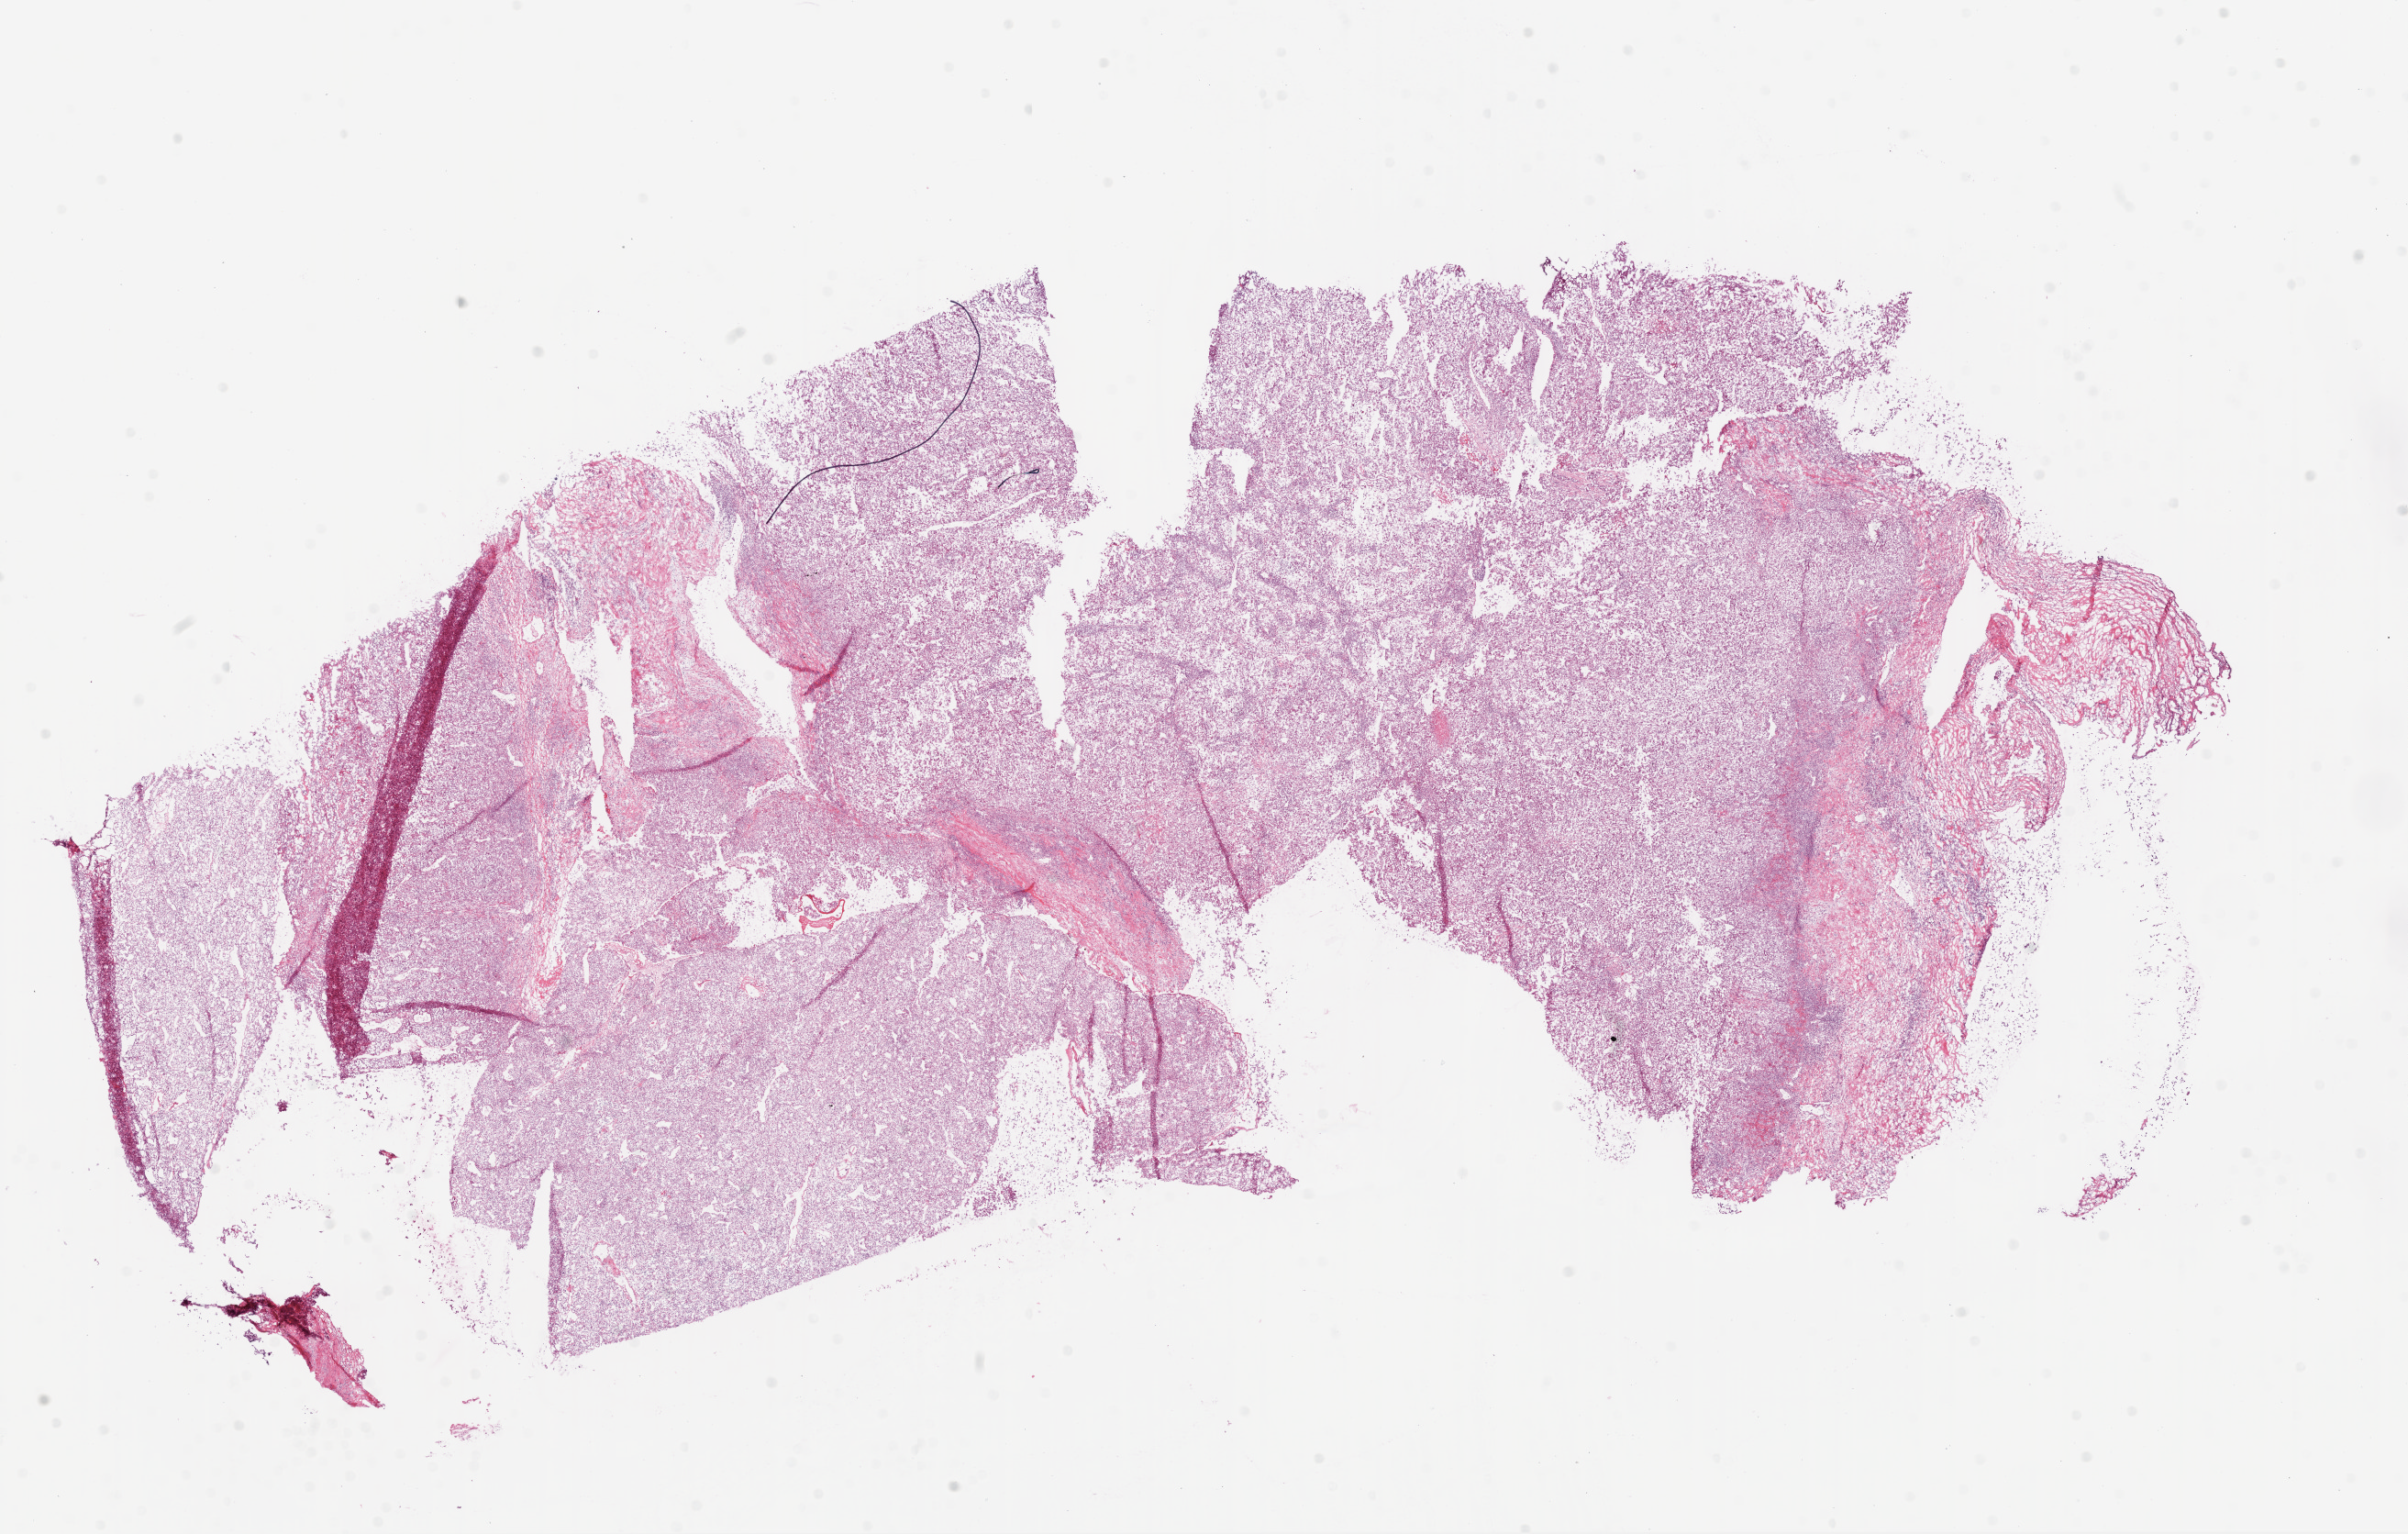
H&E whole-slide image, shown as a low-resolution overview of the whole scanned area (about 21.1 x 13.4 mm), frozen section, sample: primary tumour, kidney. Female patient; age at initial diagnosis 52 years. Slide review estimates, as recorded: tumour cells 95%, tumour nuclei 85%.
Histologic diagnosis: Clear cell adenocarcinoma, NOS.